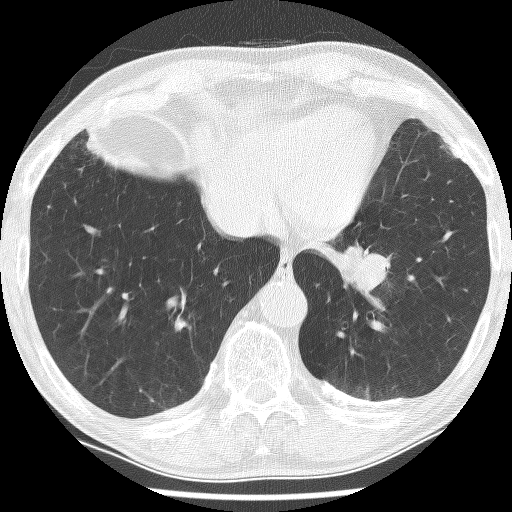
Low-dose screening chest CT, one axial slice; slice 45 of 226 in the series (ordered by position); reconstruction kernel BONE; 120 kVp; lung window (W 1500 / L -600 HU); 2.5 mm slice thickness; 512 × 512 image matrix, field of view 320 × 320 mm.
Annotated regions visible in this slice (manually delineated by an expert):
- lesion 1 (tumor, lower lobe of left lung): bounding box [x1, y1, x2, y2] px = [339, 246, 391, 298]